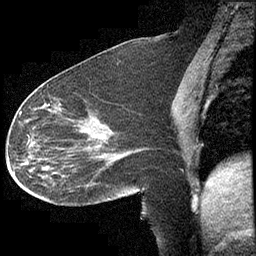
Breast MRI (dynamic contrast-enhanced), one sagittal slice; dynamic contrast-enhanced study with each time point stored as its own series, time point 2 of 4 at this slice position (early post-contrast, ordered by acquisition time); 1.5 T; TE 4.2 ms, TR 6.7 ms; 3 mm slice thickness; 256 × 256 image matrix, field of view 200 × 200 mm. Female patient, age 63 years. From the clinical record (not read from this slice): setting: breast cancer imaged before/during neoadjuvant chemotherapy; receptor status: triple-negative.
Outlined on this slice (semi-automatic segmentation, software-assisted and operator-edited):
- analysis volume of interest (the breast-tissue region the enhancement analysis was run in; not a lesion): box from (x=13, y=90) to (x=140, y=207) px
- tumour enhancement mask (voxels above the 70 % enhancement threshold inside the analysis volume of interest): (x=19, y=111)–(x=29, y=142)